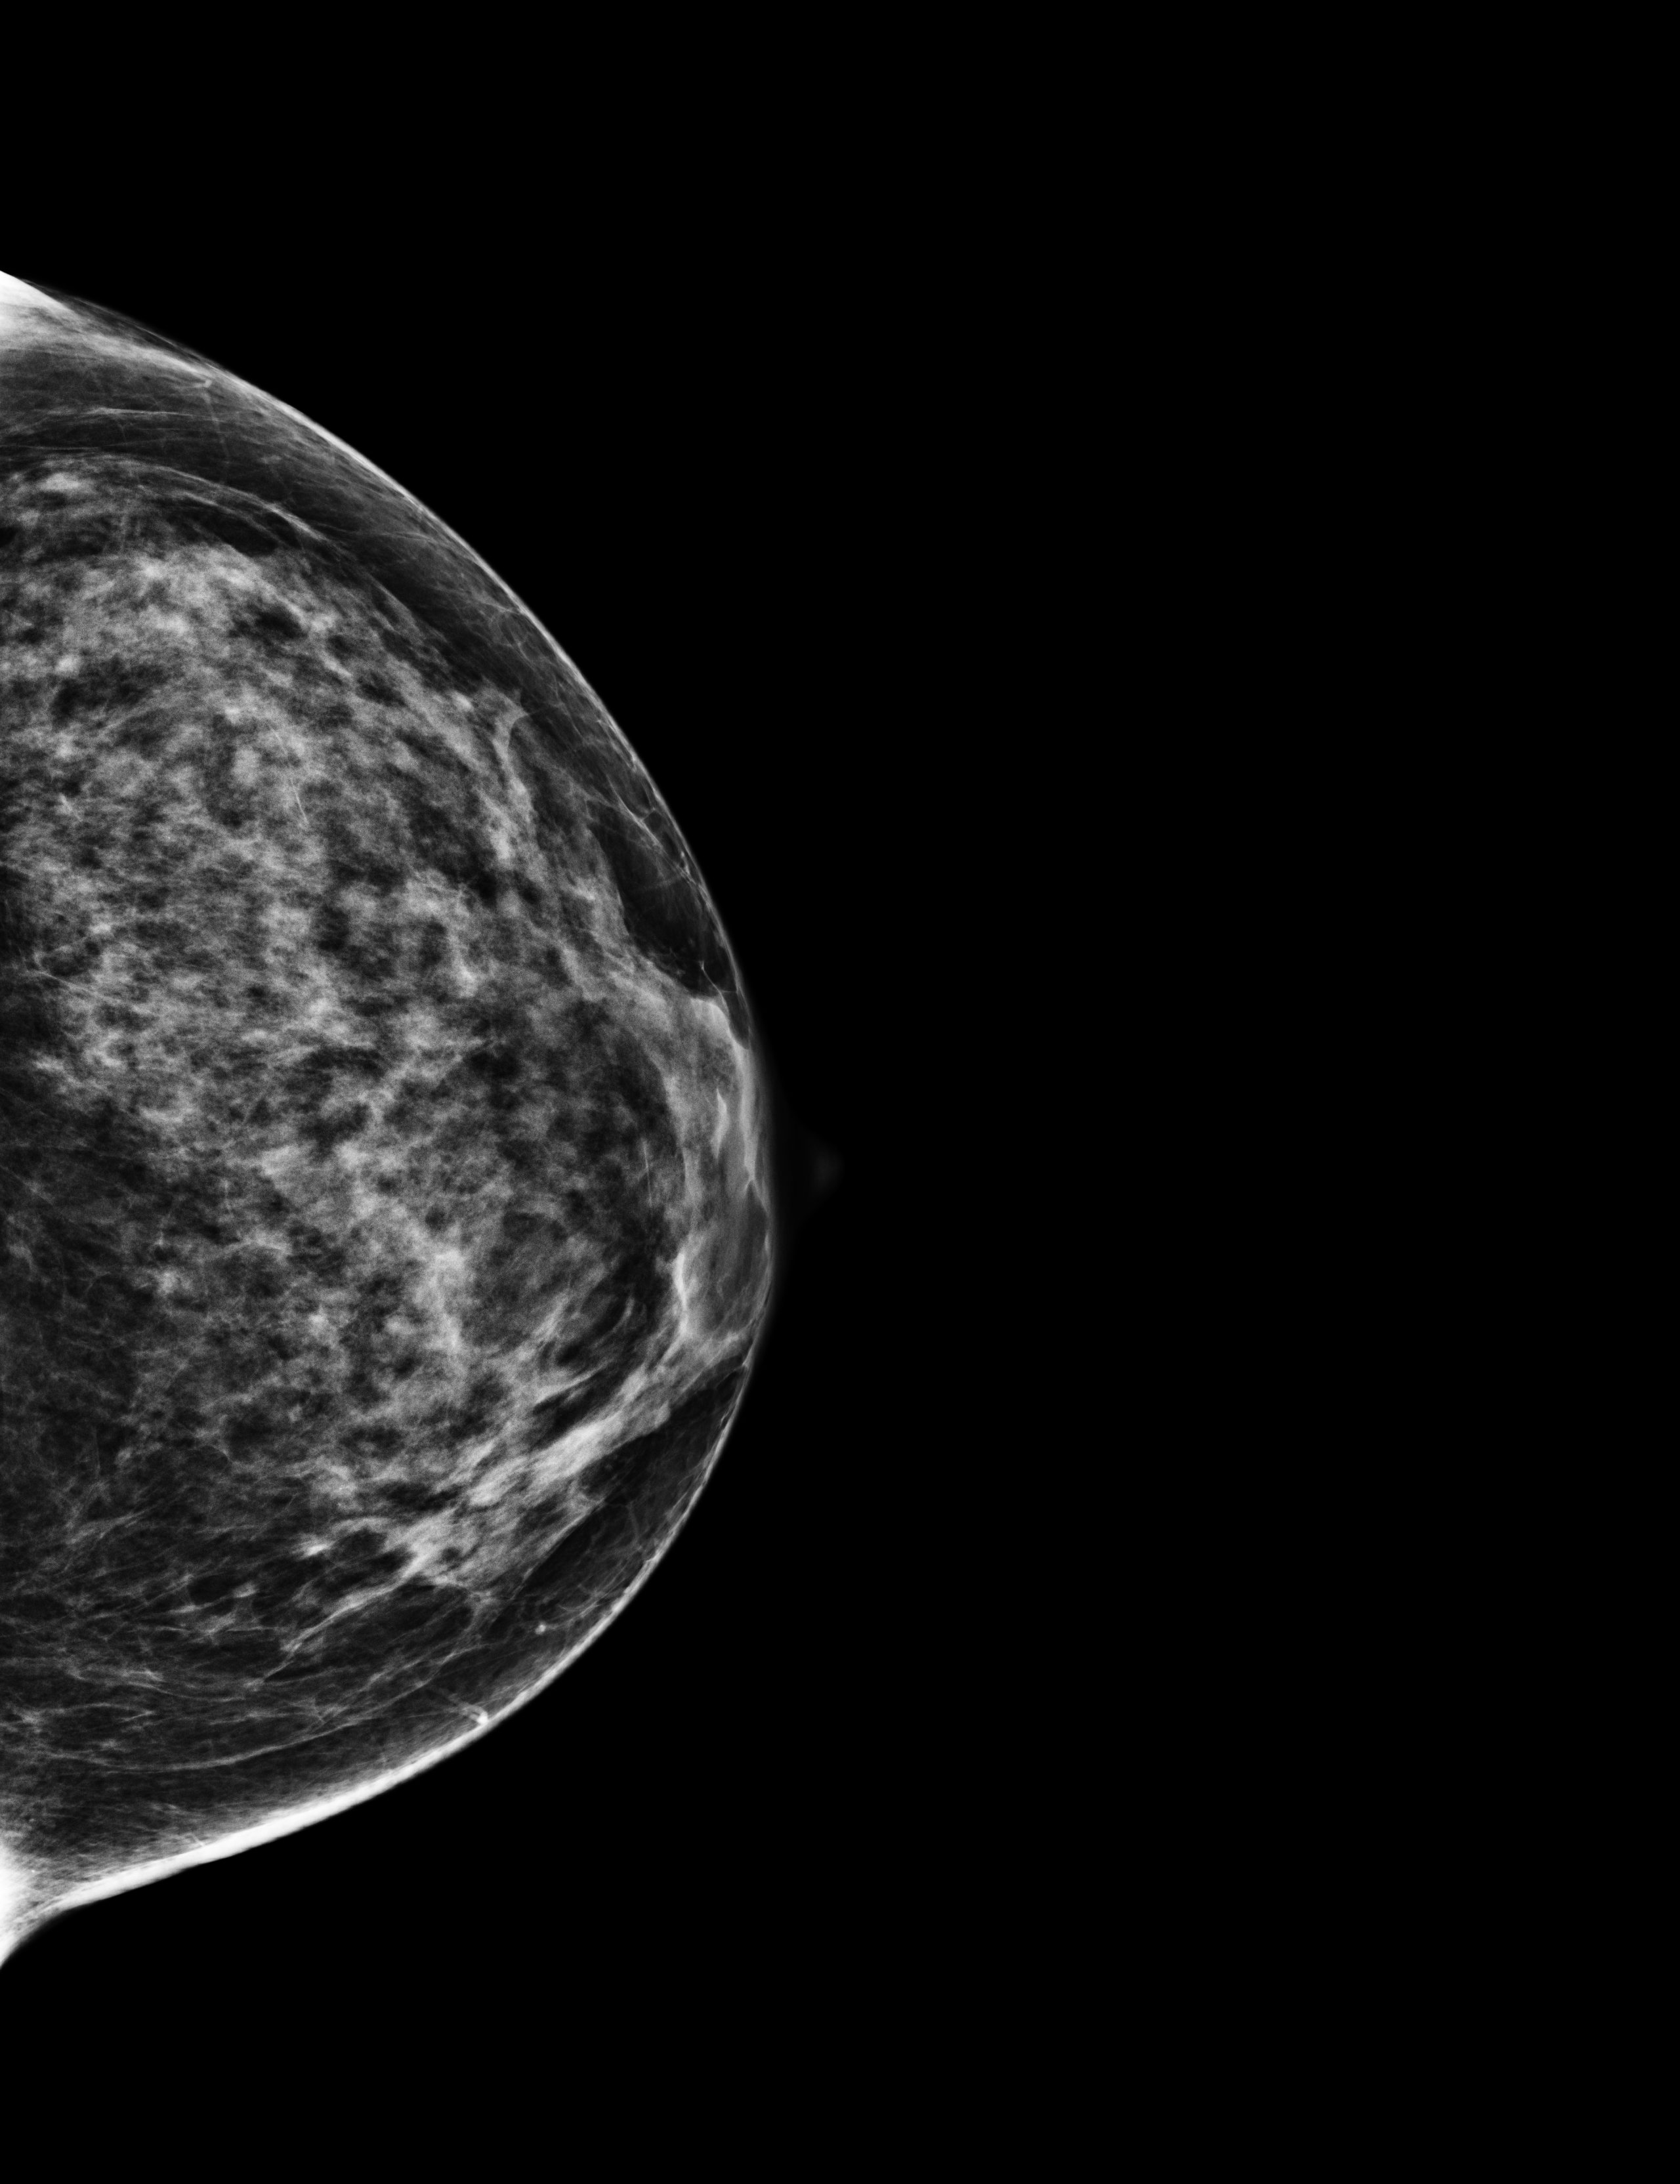
Annual screening mammography examination.
Image type: full-field digital mammogram. Breast: left. Projection: CC view.